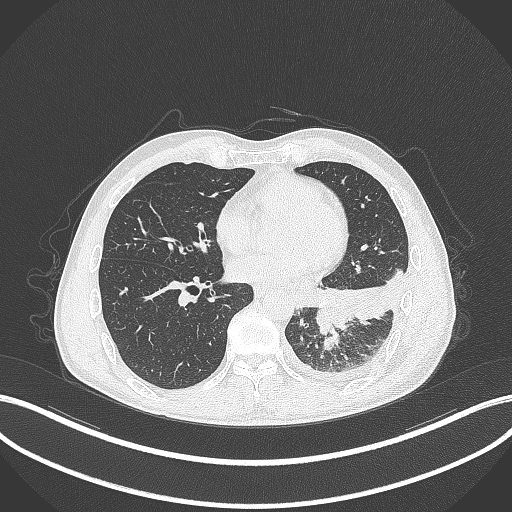
Chest CT, one axial slice; position 125 of 295 along the scan axis; 120 kVp; lung window (W 1500 / L -600 HU); 1 mm slice thickness; 512 × 512 image matrix, field of view 400 × 400 mm. Male patient, age 47 years. Case-level facts recorded for this patient, not image findings: clinical TNM (as recorded): T3 N1 M1c; histopathological grade: G3.
Annotated regions visible in this slice (bounding box drawn by a radiologist):
- lung tumour (recorded histology: small cell carcinoma): bounding box (x1, y1, x2, y2) in pixels: (314, 301, 352, 335)